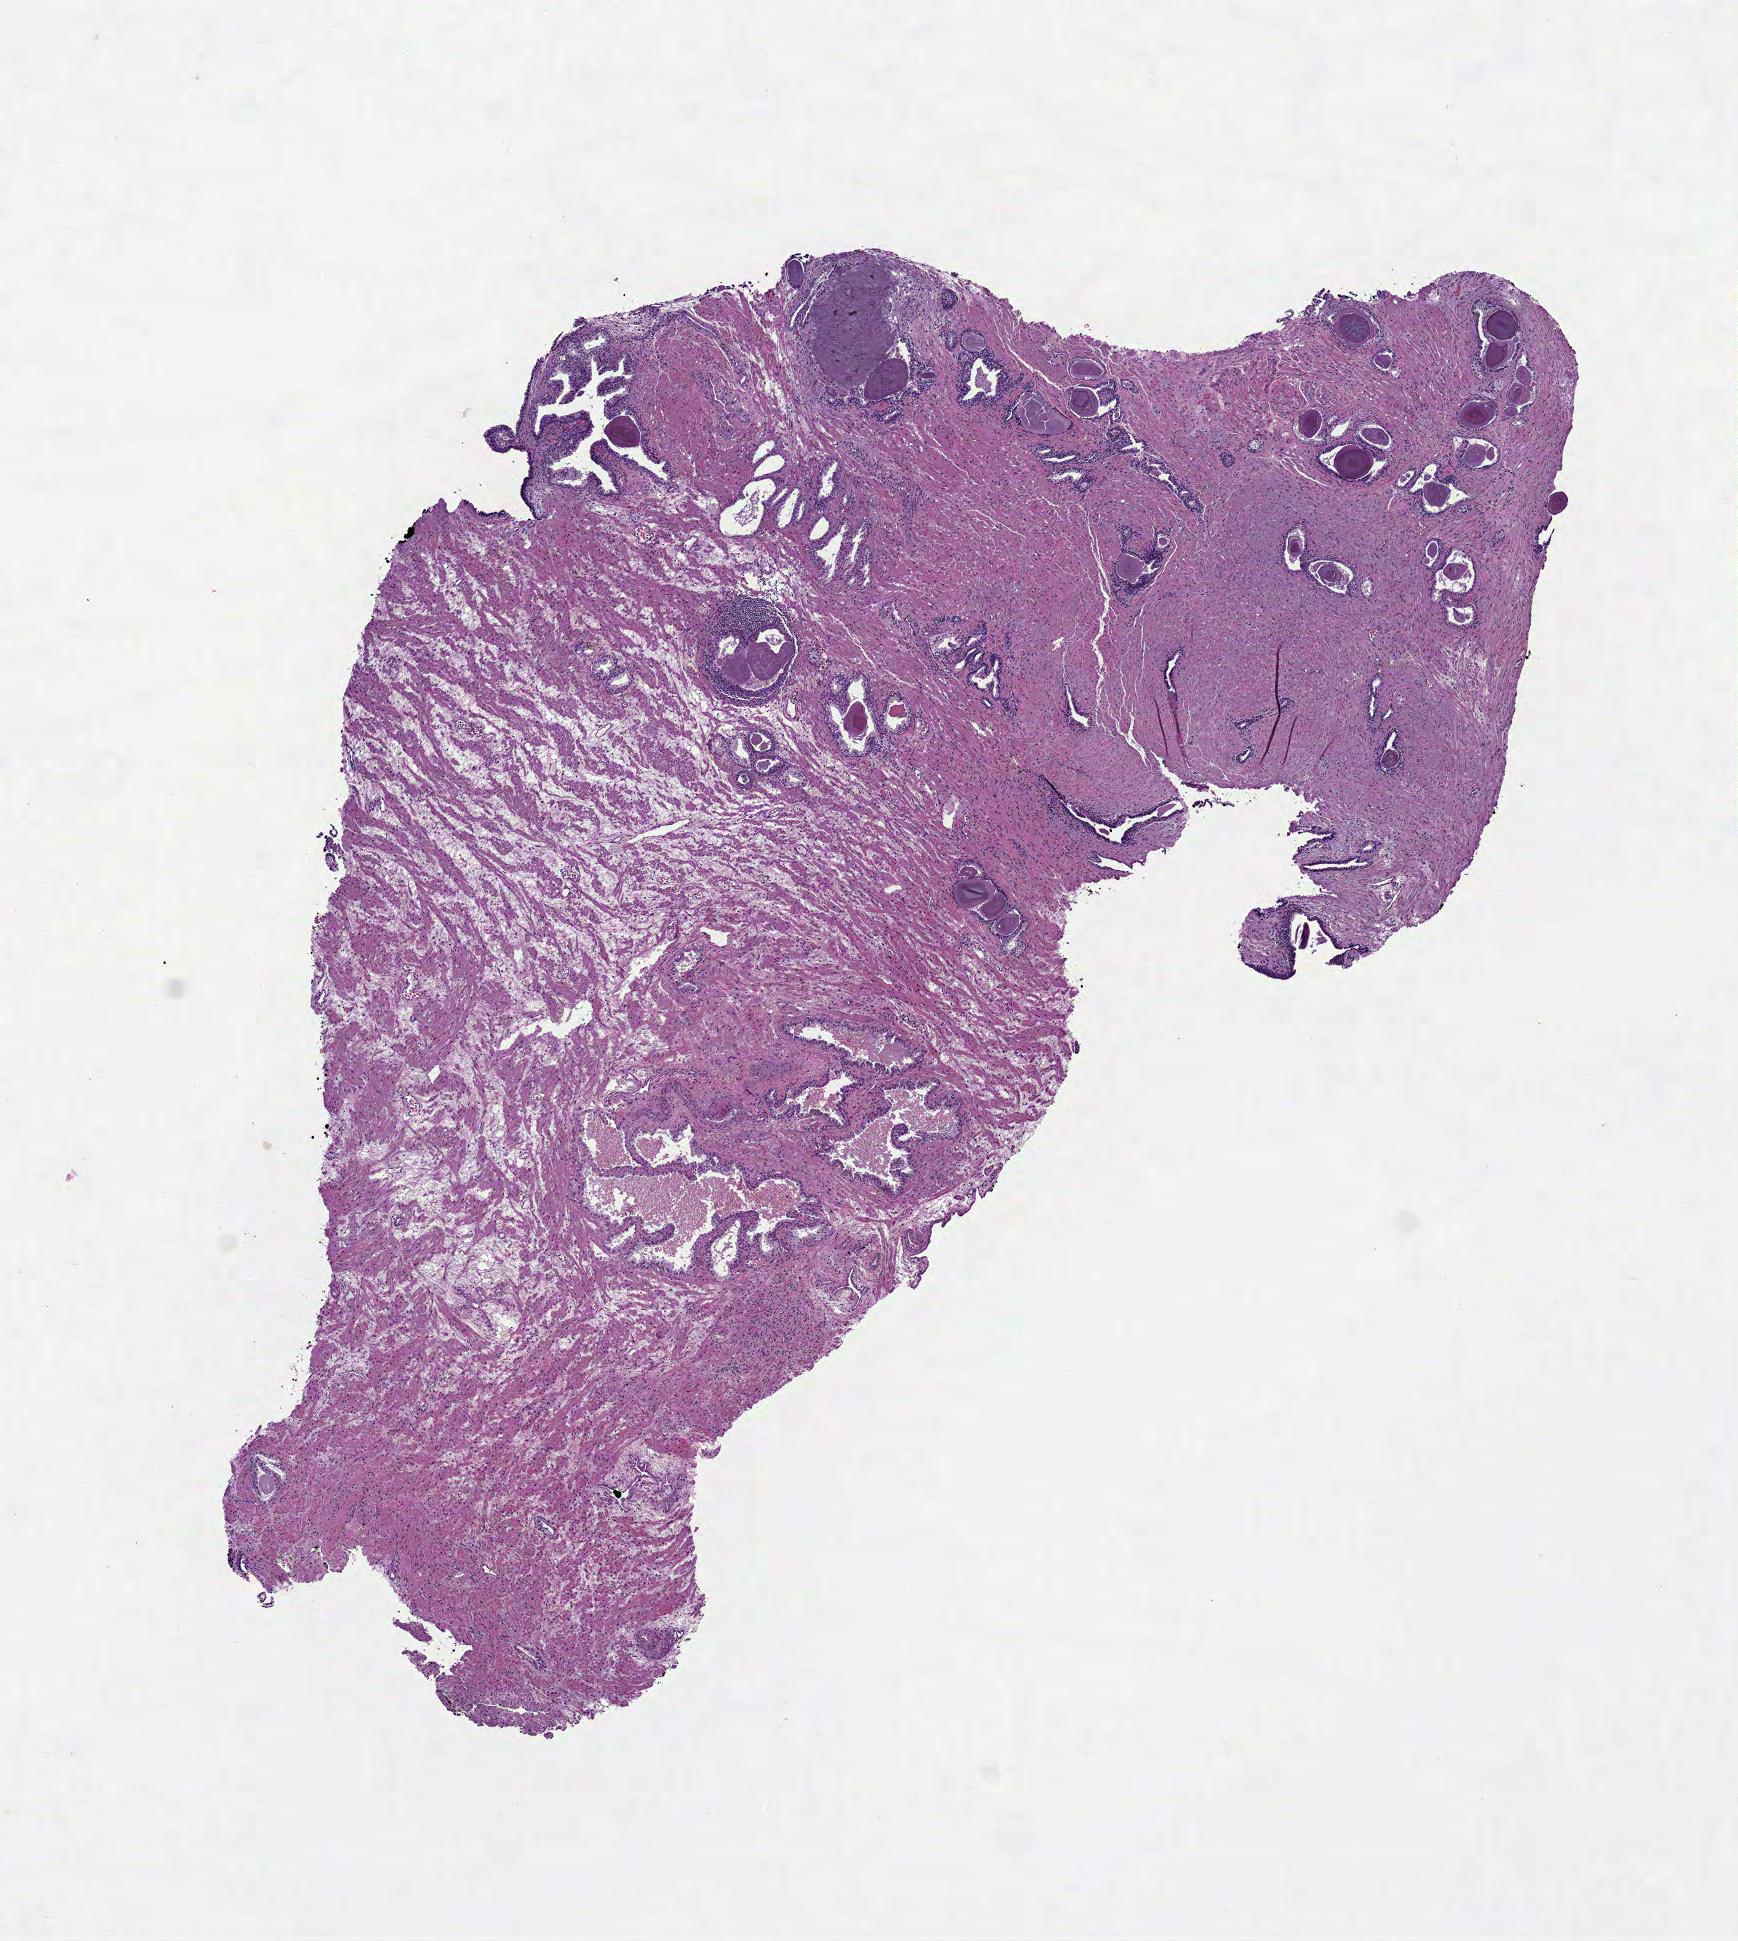
Whole-slide histology image, H&E, low-resolution overview of the scanned area, about 7.0 x 7.8 mm (slide scanned at 40x); formalin-fixed paraffin-embedded (FFPE) diagnostic section; primary tumour sample from the prostate. Patient: male, age at initial diagnosis 70 years. Gleason score: 7 (3+4).
Pathologic diagnosis: Adenocarcinoma, NOS (prostate gland).